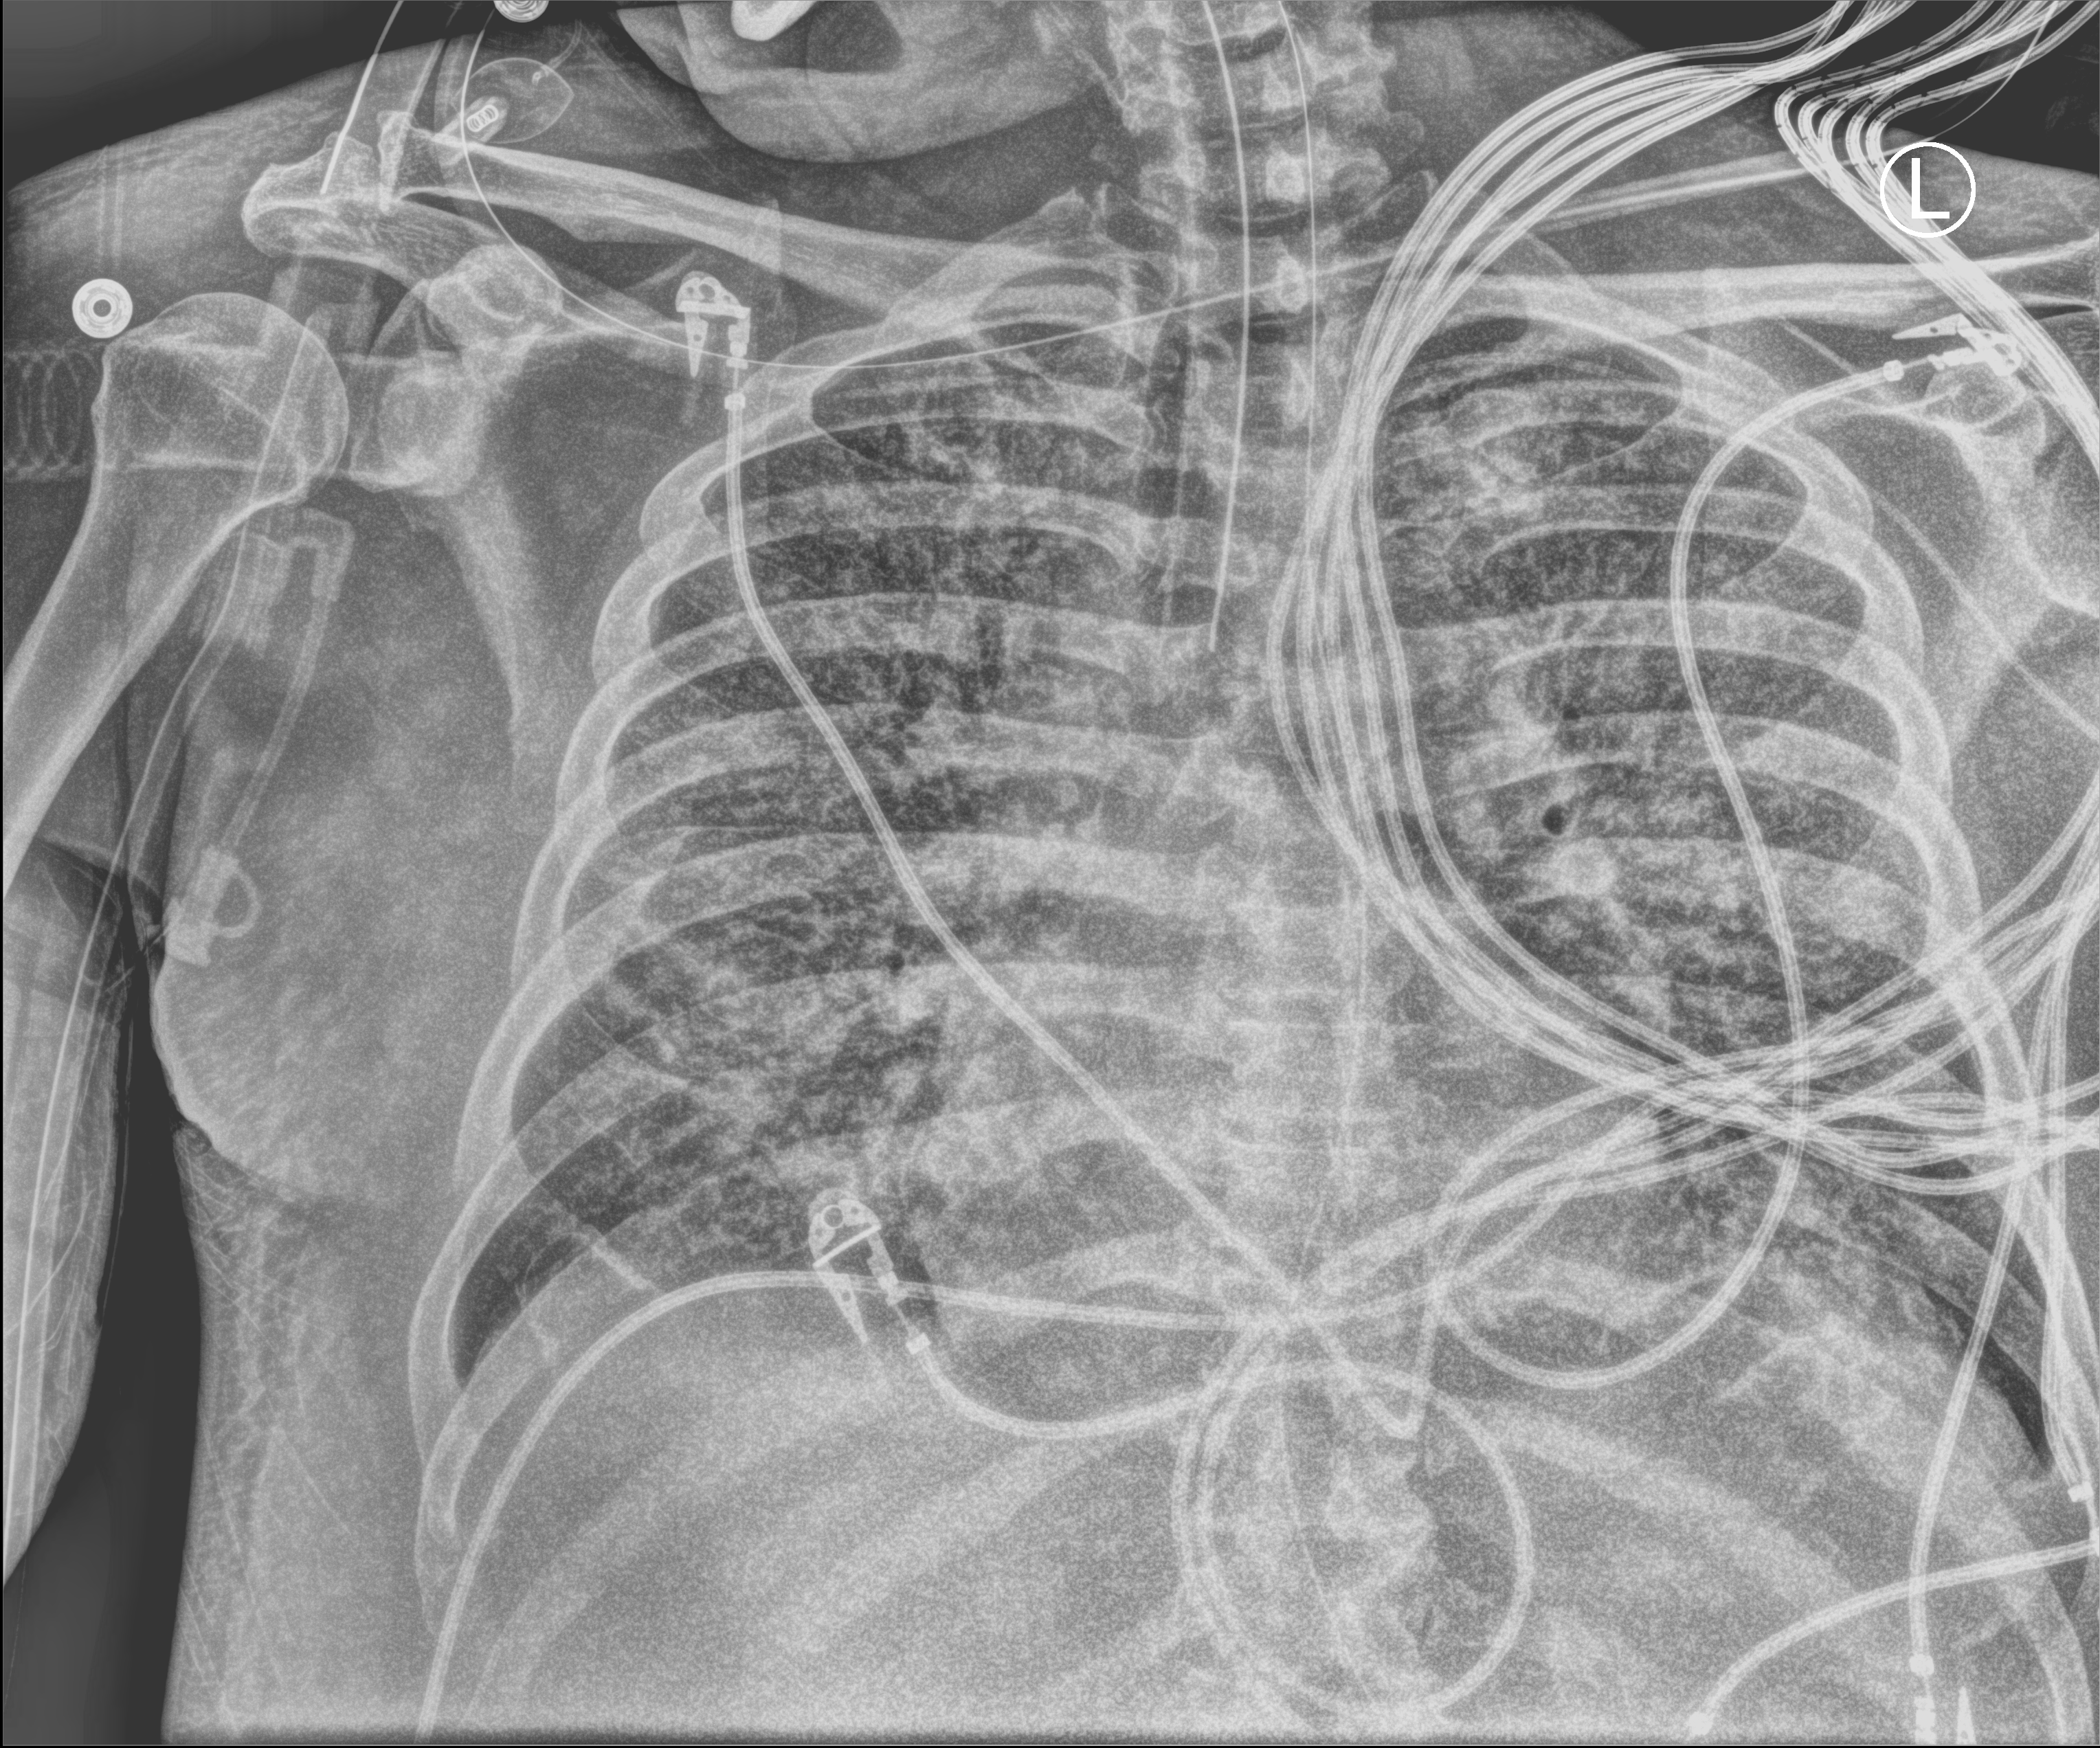
Chest X-ray (portable). Male patient hospitalised with COVID-19, age 60–74 years.
From the hospital-stay record, not from the radiograph (when in the stay this image was taken is not recorded):
- hypertension (admission record): yes
- COPD (admission record): no
- chronic kidney disease (admission record): no